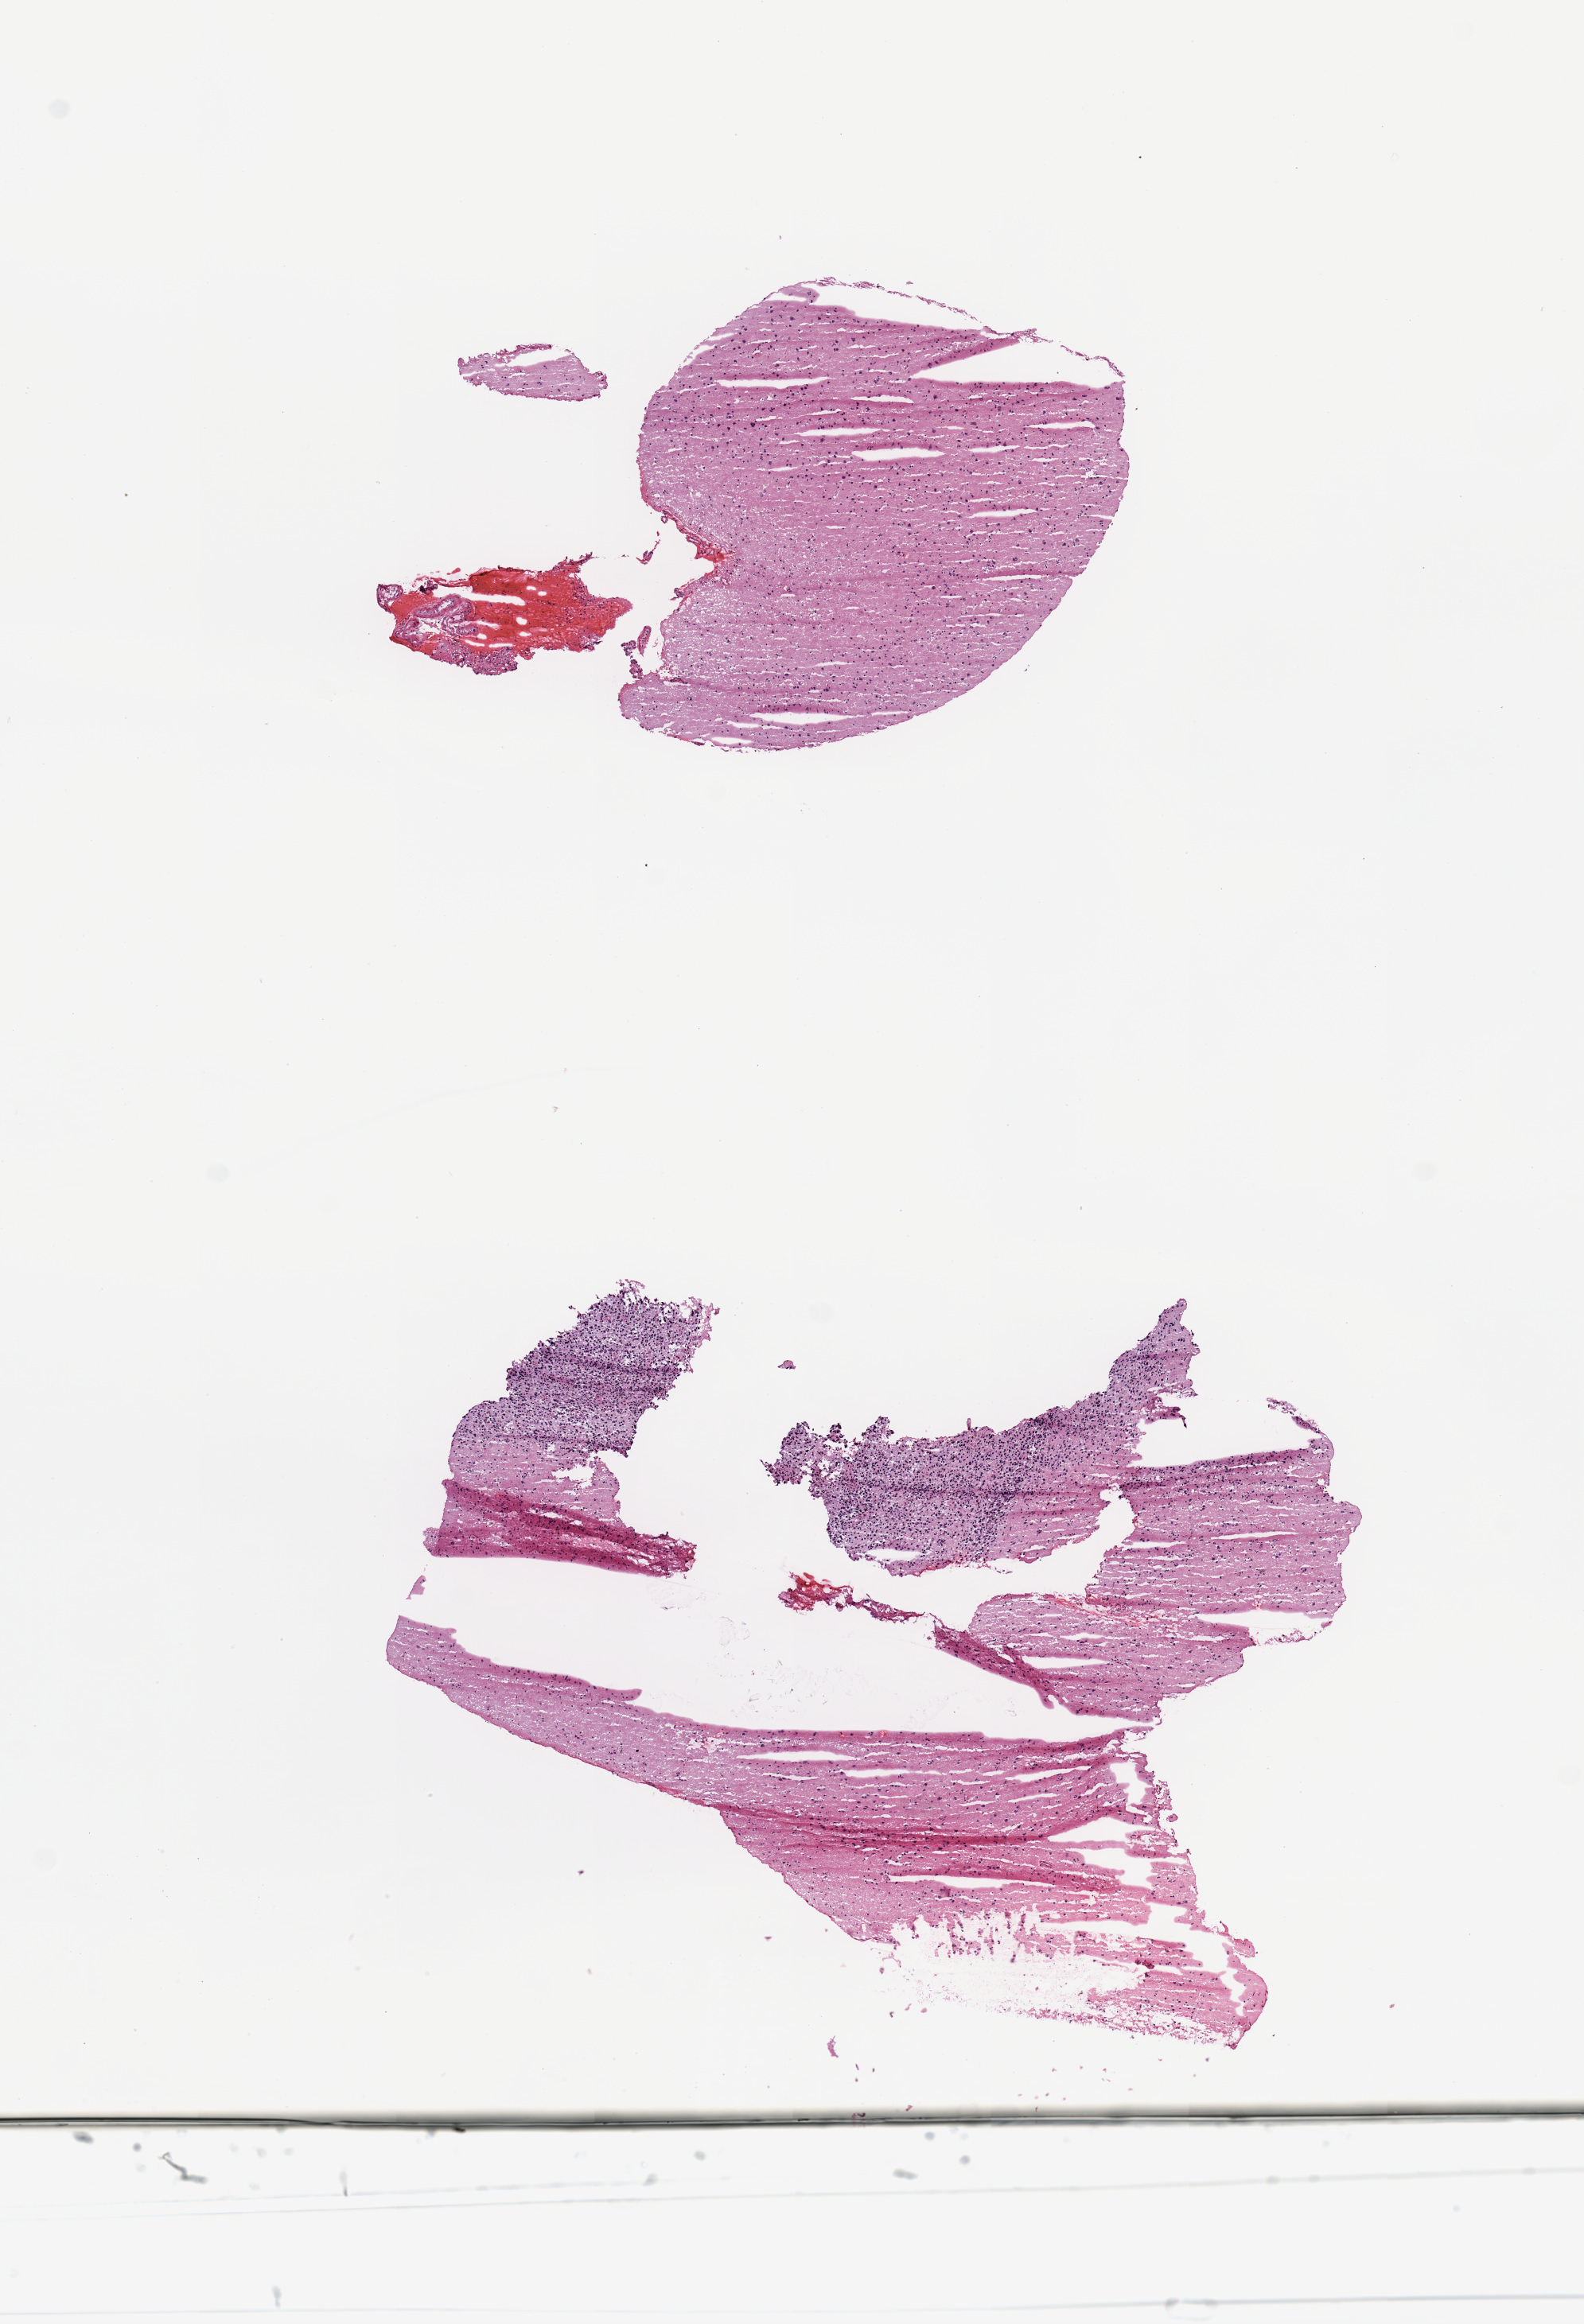
Digitized H&E tissue section (whole slide), low-resolution overview of the scanned area, about 7.9 x 11.6 mm (slide scanned at 20x). Tumour tissue sample, brain. Patient: male, age 61 years.
Patient diagnosis (cohort enrolment): glioblastoma multiforme (brain). Primary tumour site (as recorded): temporal lobe.